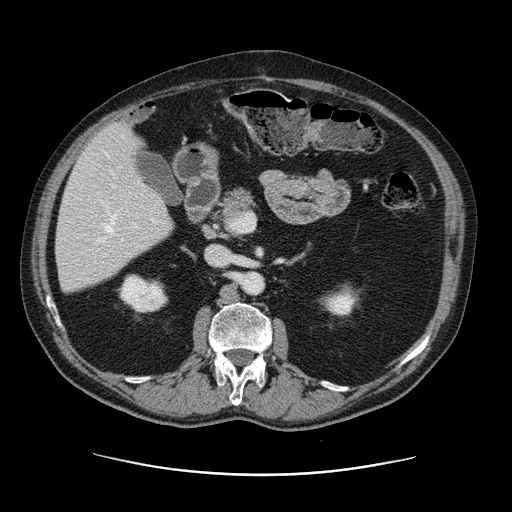
Contrast-enhanced abdominal CT, one axial slice; position 61 of 141 along the scan axis; intravenous contrast given; soft-tissue window (W 400 / L 40 HU); 2.5 mm slice thickness; 512 × 512 image matrix. Male patient, age 72 years. From the clinical record (not read from this slice): diagnosis: colorectal cancer liver metastases, imaged before liver resection; multiple liver metastases: yes; largest metastasis: 5.4 cm; chemotherapy before resection: yes.
Outlined on this slice (outlined manually by an expert reader):
- hepatic veins: bounding box [x1, y1, x2, y2] px = [98, 135, 124, 242]
- liver: [57, 124, 173, 293]
- planned liver remnant (the part of the liver to remain after resection): [57, 184, 173, 293]
- portal vein (with intrahepatic branches): [106, 206, 140, 229]